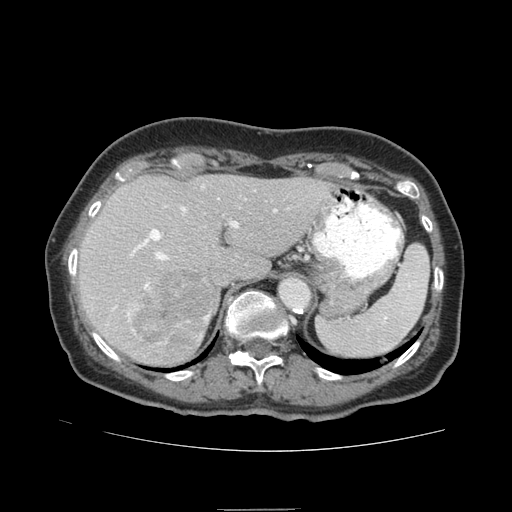
Contrast-enhanced abdominal CT (liver protocol), one axial slice. Slice 57 of 95 in the series (ordered by position). Reconstruction kernel STANDARD. 140 kVp. Soft-tissue window (W 400 / L 40 HU). 512 × 512 image matrix. Case-level facts recorded for this patient, not image findings: diagnosis: hepatocellular carcinoma (patient treated with transarterial chemoembolisation; whether this scan precedes or follows treatment is not stated here); TNM stage (as recorded): Stage-IVA.
Annotated regions visible in this slice (semi-automatic segmentation, software-assisted and operator-edited):
- liver parenchyma outside the tumour (the mass and vessels are separate outlines, so this box may not span the whole liver): bounding box (x1, y1, x2, y2) in pixels: (78, 174, 332, 364)
- mass: (127, 267, 217, 358)
- liver vessels: (112, 207, 277, 316)